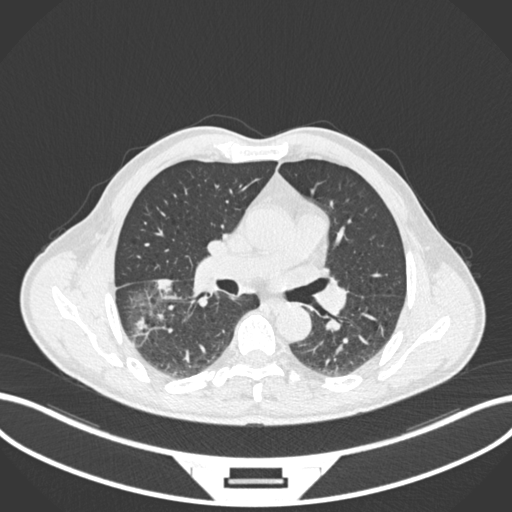
Chest CT, one axial slice; slice 110 of 208 in the series (ordered by position); reconstruction kernel B30f; 120 kVp; lung window (W 1500 / L -600 HU); 1 mm slice thickness; 512 × 512 image matrix, field of view 400 × 400 mm. Male patient, age 58 years. From the clinical record (not read from this slice): clinical TNM (as recorded): T3 N0 M0; histopathological grade: G2.
Outlined on this slice (bounding box drawn by a radiologist):
- lung tumour (recorded histology: squamous cell carcinoma): box from (x=134, y=277) to (x=174, y=332) px